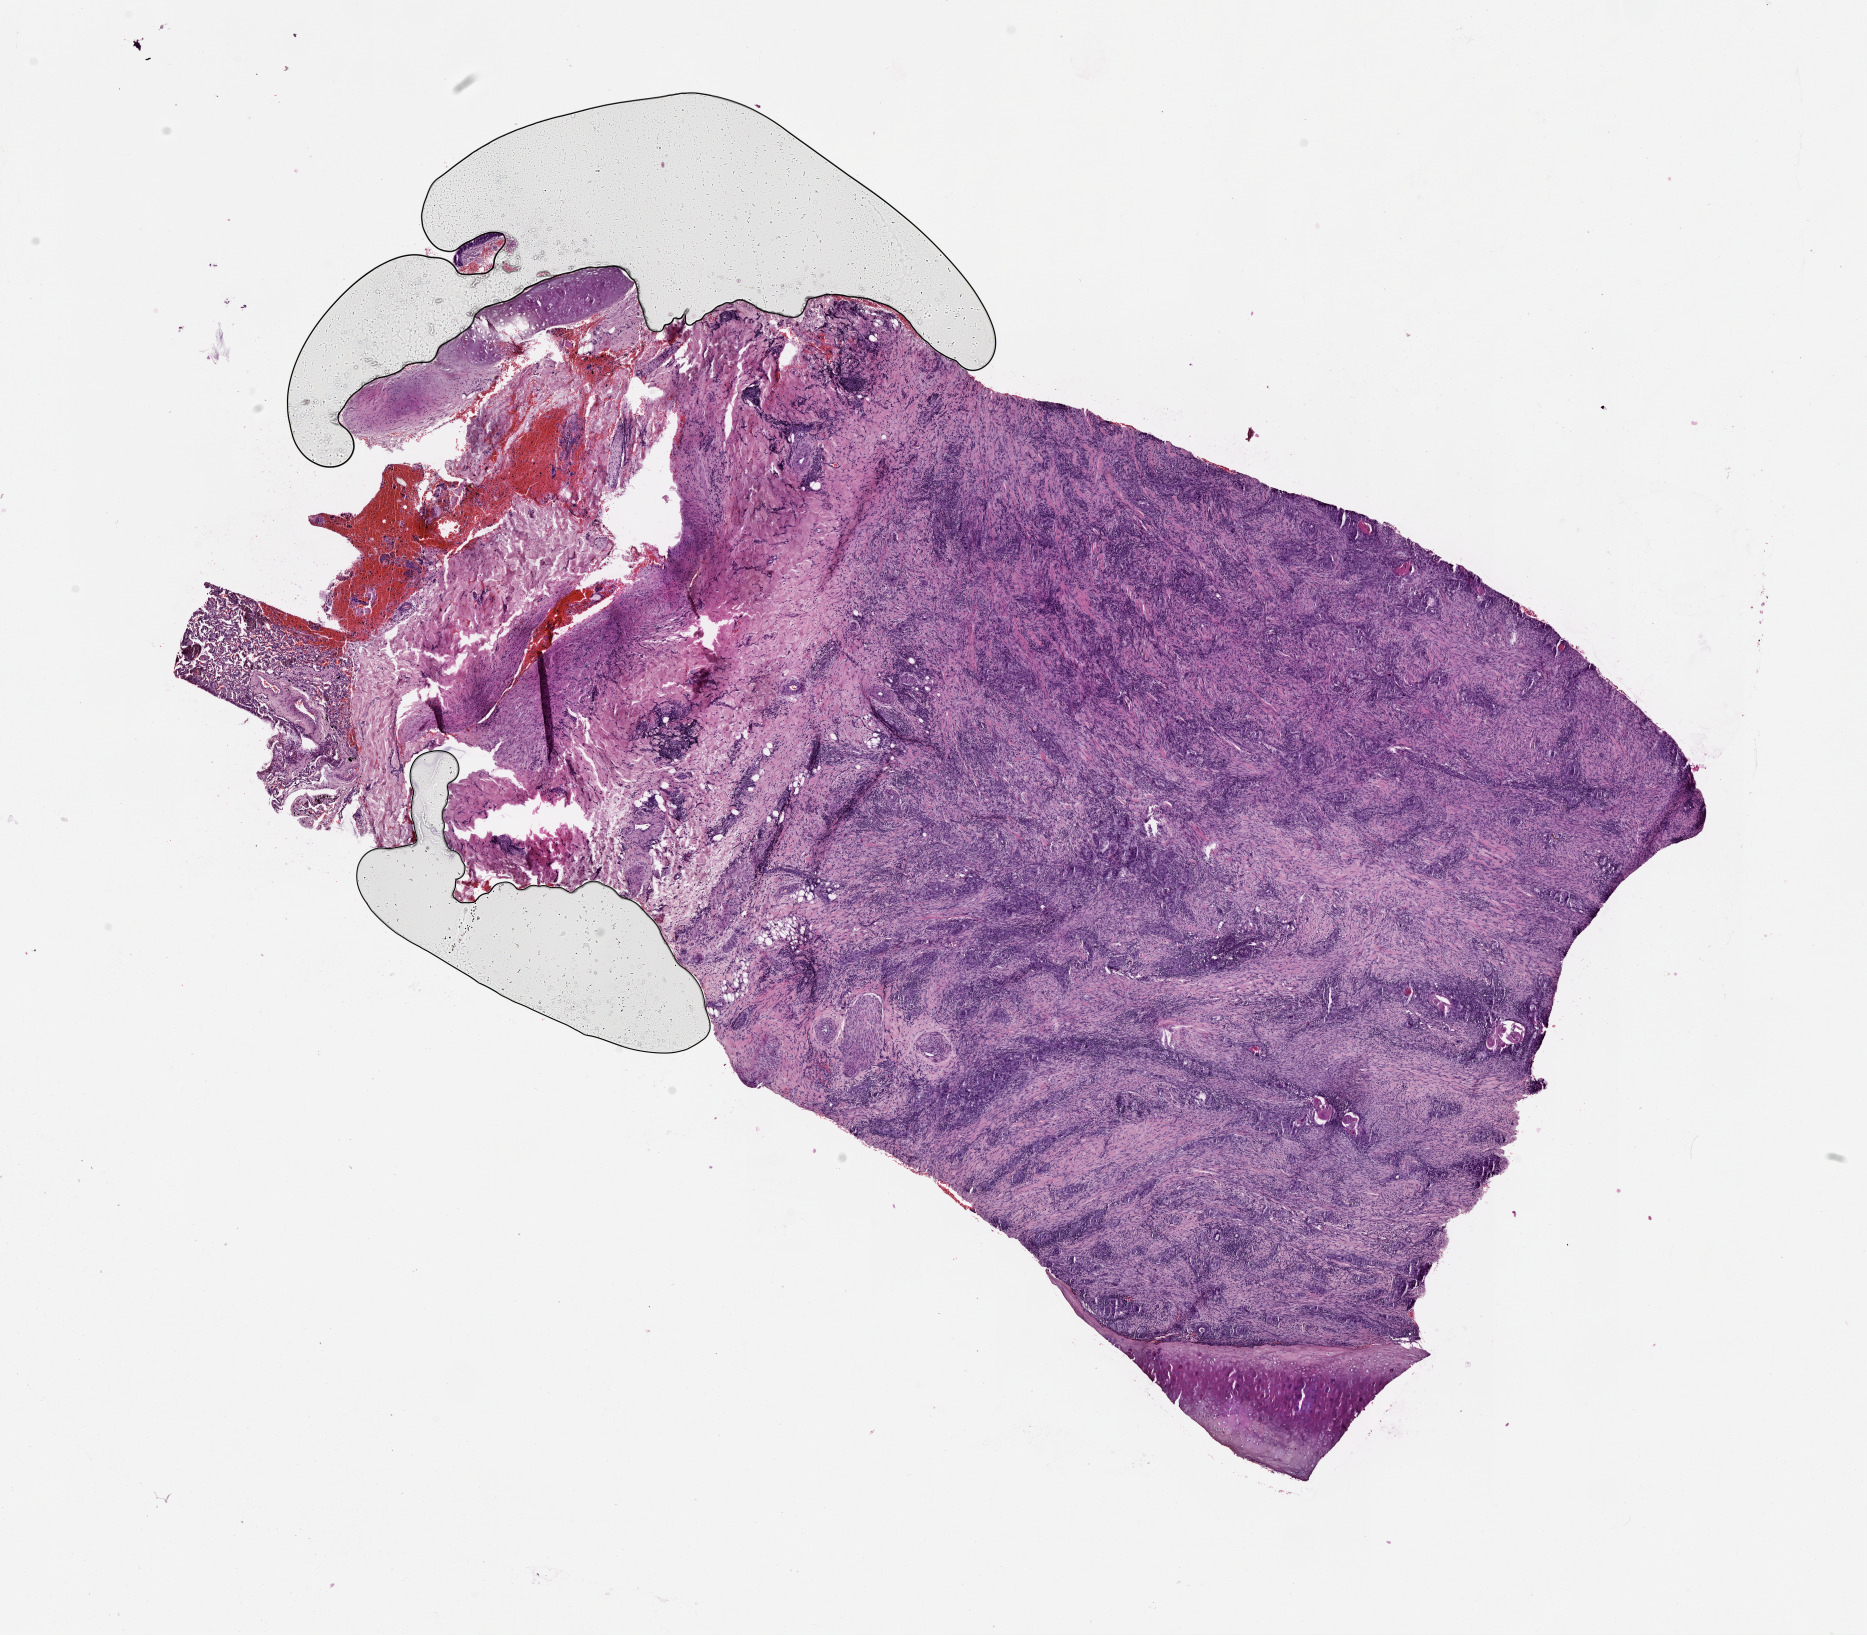
Hematoxylin and eosin (H&E) stained whole-slide image, low-resolution overview of the scanned area, about 15.0 x 13.2 mm (slide scanned at 20x), tumour tissue sample, lung. Female, 56 y/o.
- patient diagnosis (cohort enrolment): squamous cell carcinoma (lung)